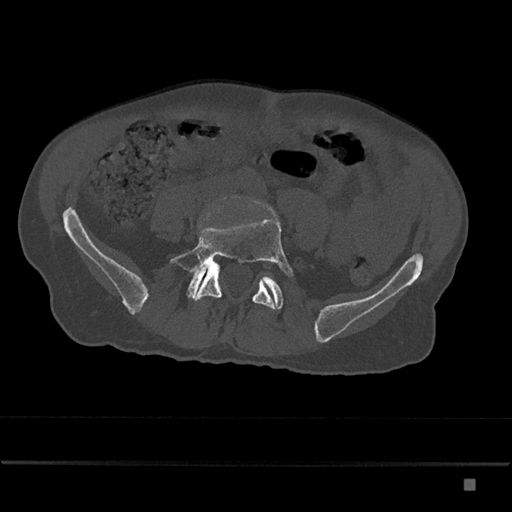
CT including the spine, one axial slice; position 276 of 797 along the scan axis; reconstruction kernel Br40s/3; 120 kVp; bone window (W 1800 / L 400 HU); 512 × 512 image matrix. Male patient, age 72 years. From the clinical record (not read from this slice): primary cancer: prostate.
Outlined on this slice (semi-automatically segmented with operator editing):
- L5 vertebra: bounding box (x1, y1, x2, y2) in pixels: (169, 219, 293, 309)